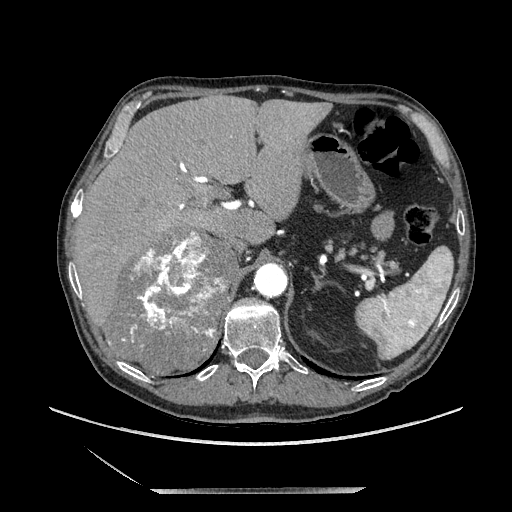
Contrast-enhanced abdominal CT, one axial slice. Slice 148 of 243 in the series (ordered by position). Soft-tissue window (W 400 / L 40 HU). 1.25 mm slice thickness. 512 × 512 image matrix, field of view 420 × 420 mm. Male patient. From the clinical record (not read from this slice): diagnosis: adrenocortical carcinoma; tumour side: right adrenal; tumour size at pathology: 16 cm; Ki-67 index: 17 %; stage (as recorded): 3.
Structures marked on this image (semi-automatically segmented with operator editing):
- mass: bounding box (x1, y1, x2, y2) in pixels: (109, 231, 234, 373)